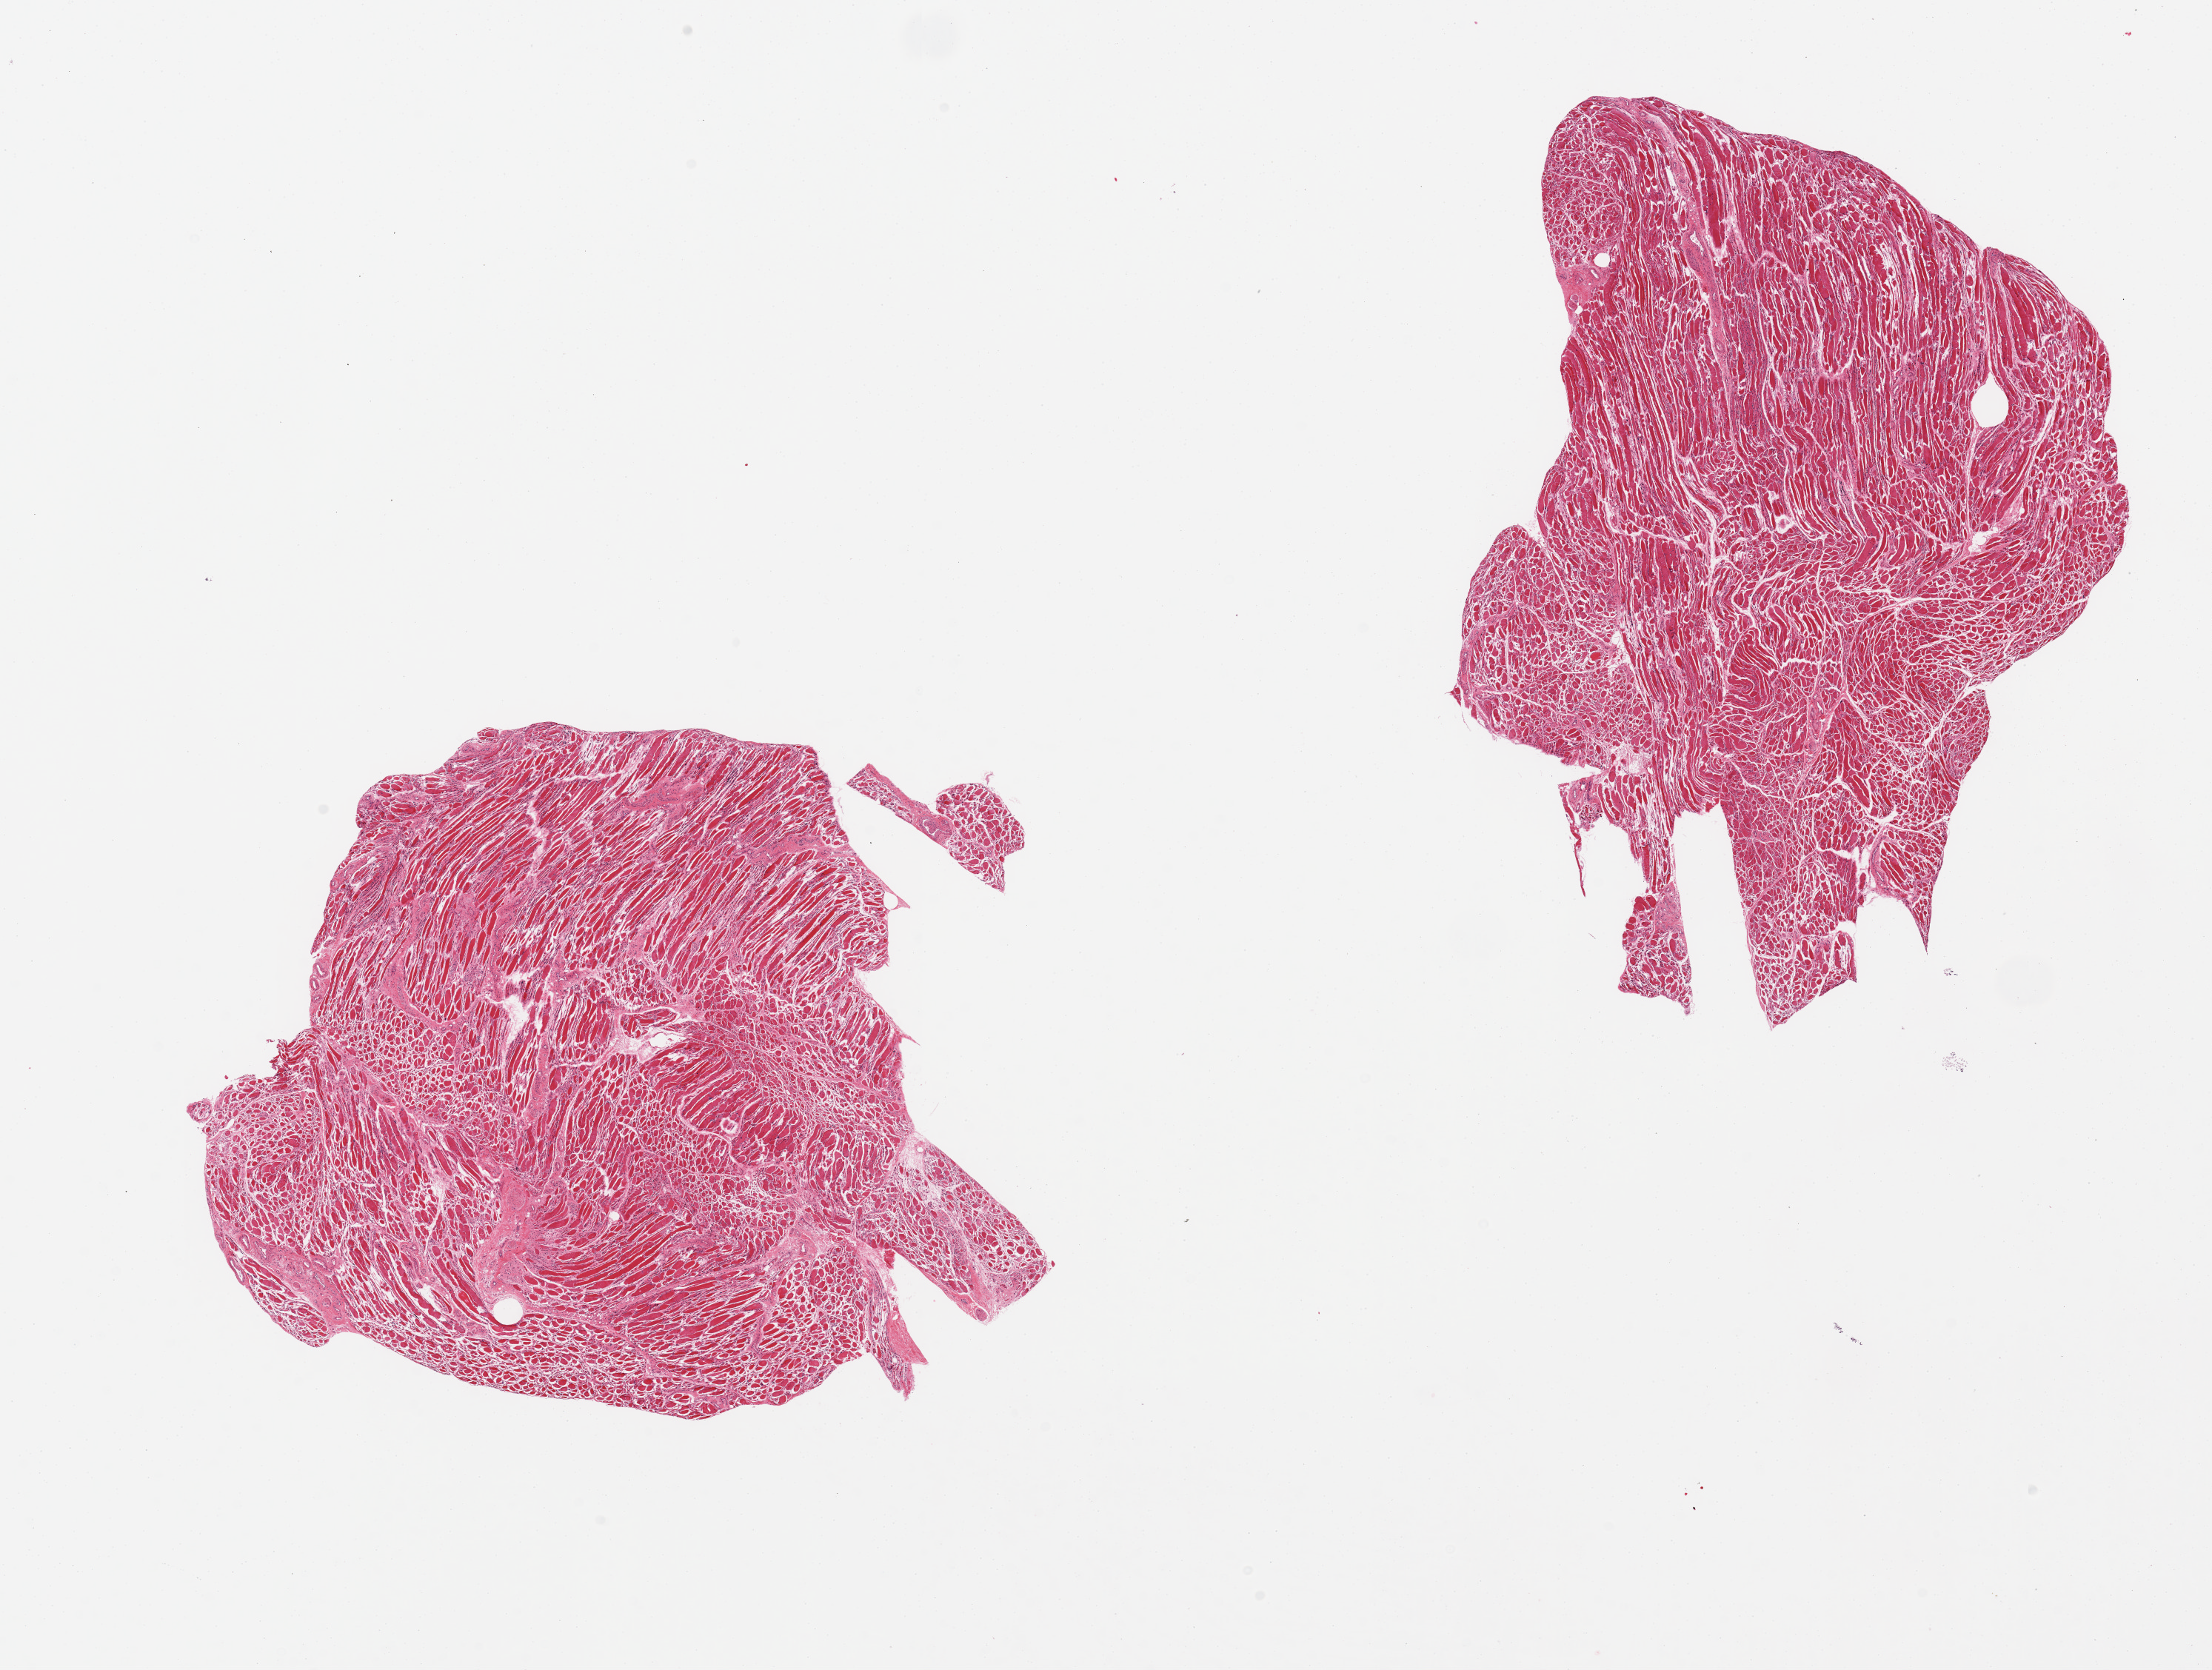
Digitized H&E-stained section, brightfield — shown as a low-resolution overview of the whole scanned area (about 23.6 x 17.8 mm); PAXgene-fixed, paraffin-embedded tissue; sampled site (target tissue): skeletal muscle; donor tissue sample. Male donor.
- pathologist's review note for this sample: 2 pieces; fibrillar atrophy; appears edematous, minimal interstitial fat